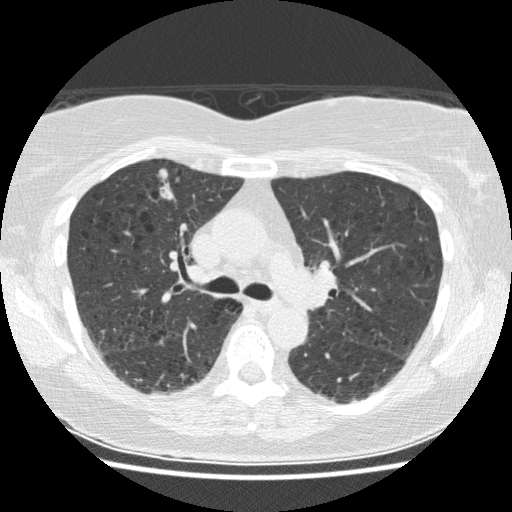
Low-dose screening chest CT, axial slice. Baseline screening round. Lung window (W 1500 / L -600 HU). 512 × 512 image matrix. Female, age 63 years at enrolment. Current smoker at enrolment.
Expert reader's lesion annotation, bounding box <143,158,183,208> (left, top, right, bottom; pixels). Screening reader's record for this exam (one nodule recorded; not confirmed to be the boxed lesion): non-calcified nodule or mass ≥4 mm, right upper lobe, 18 × 14 mm, spiculated (stellate) margins, soft tissue attenuation. Official screen result: positive, change unspecified: nodule(s) >= 4 mm or enlarging nodule(s), mass(es), or other non-specific abnormalities suspicious for lung cancer. Lung cancer was diagnosed 87 days after this screen: papillary adenocarcinoma, NOS, right upper lobe, well differentiated (G1), stage IA (AJCC 6th edition), 19 mm at pathology.